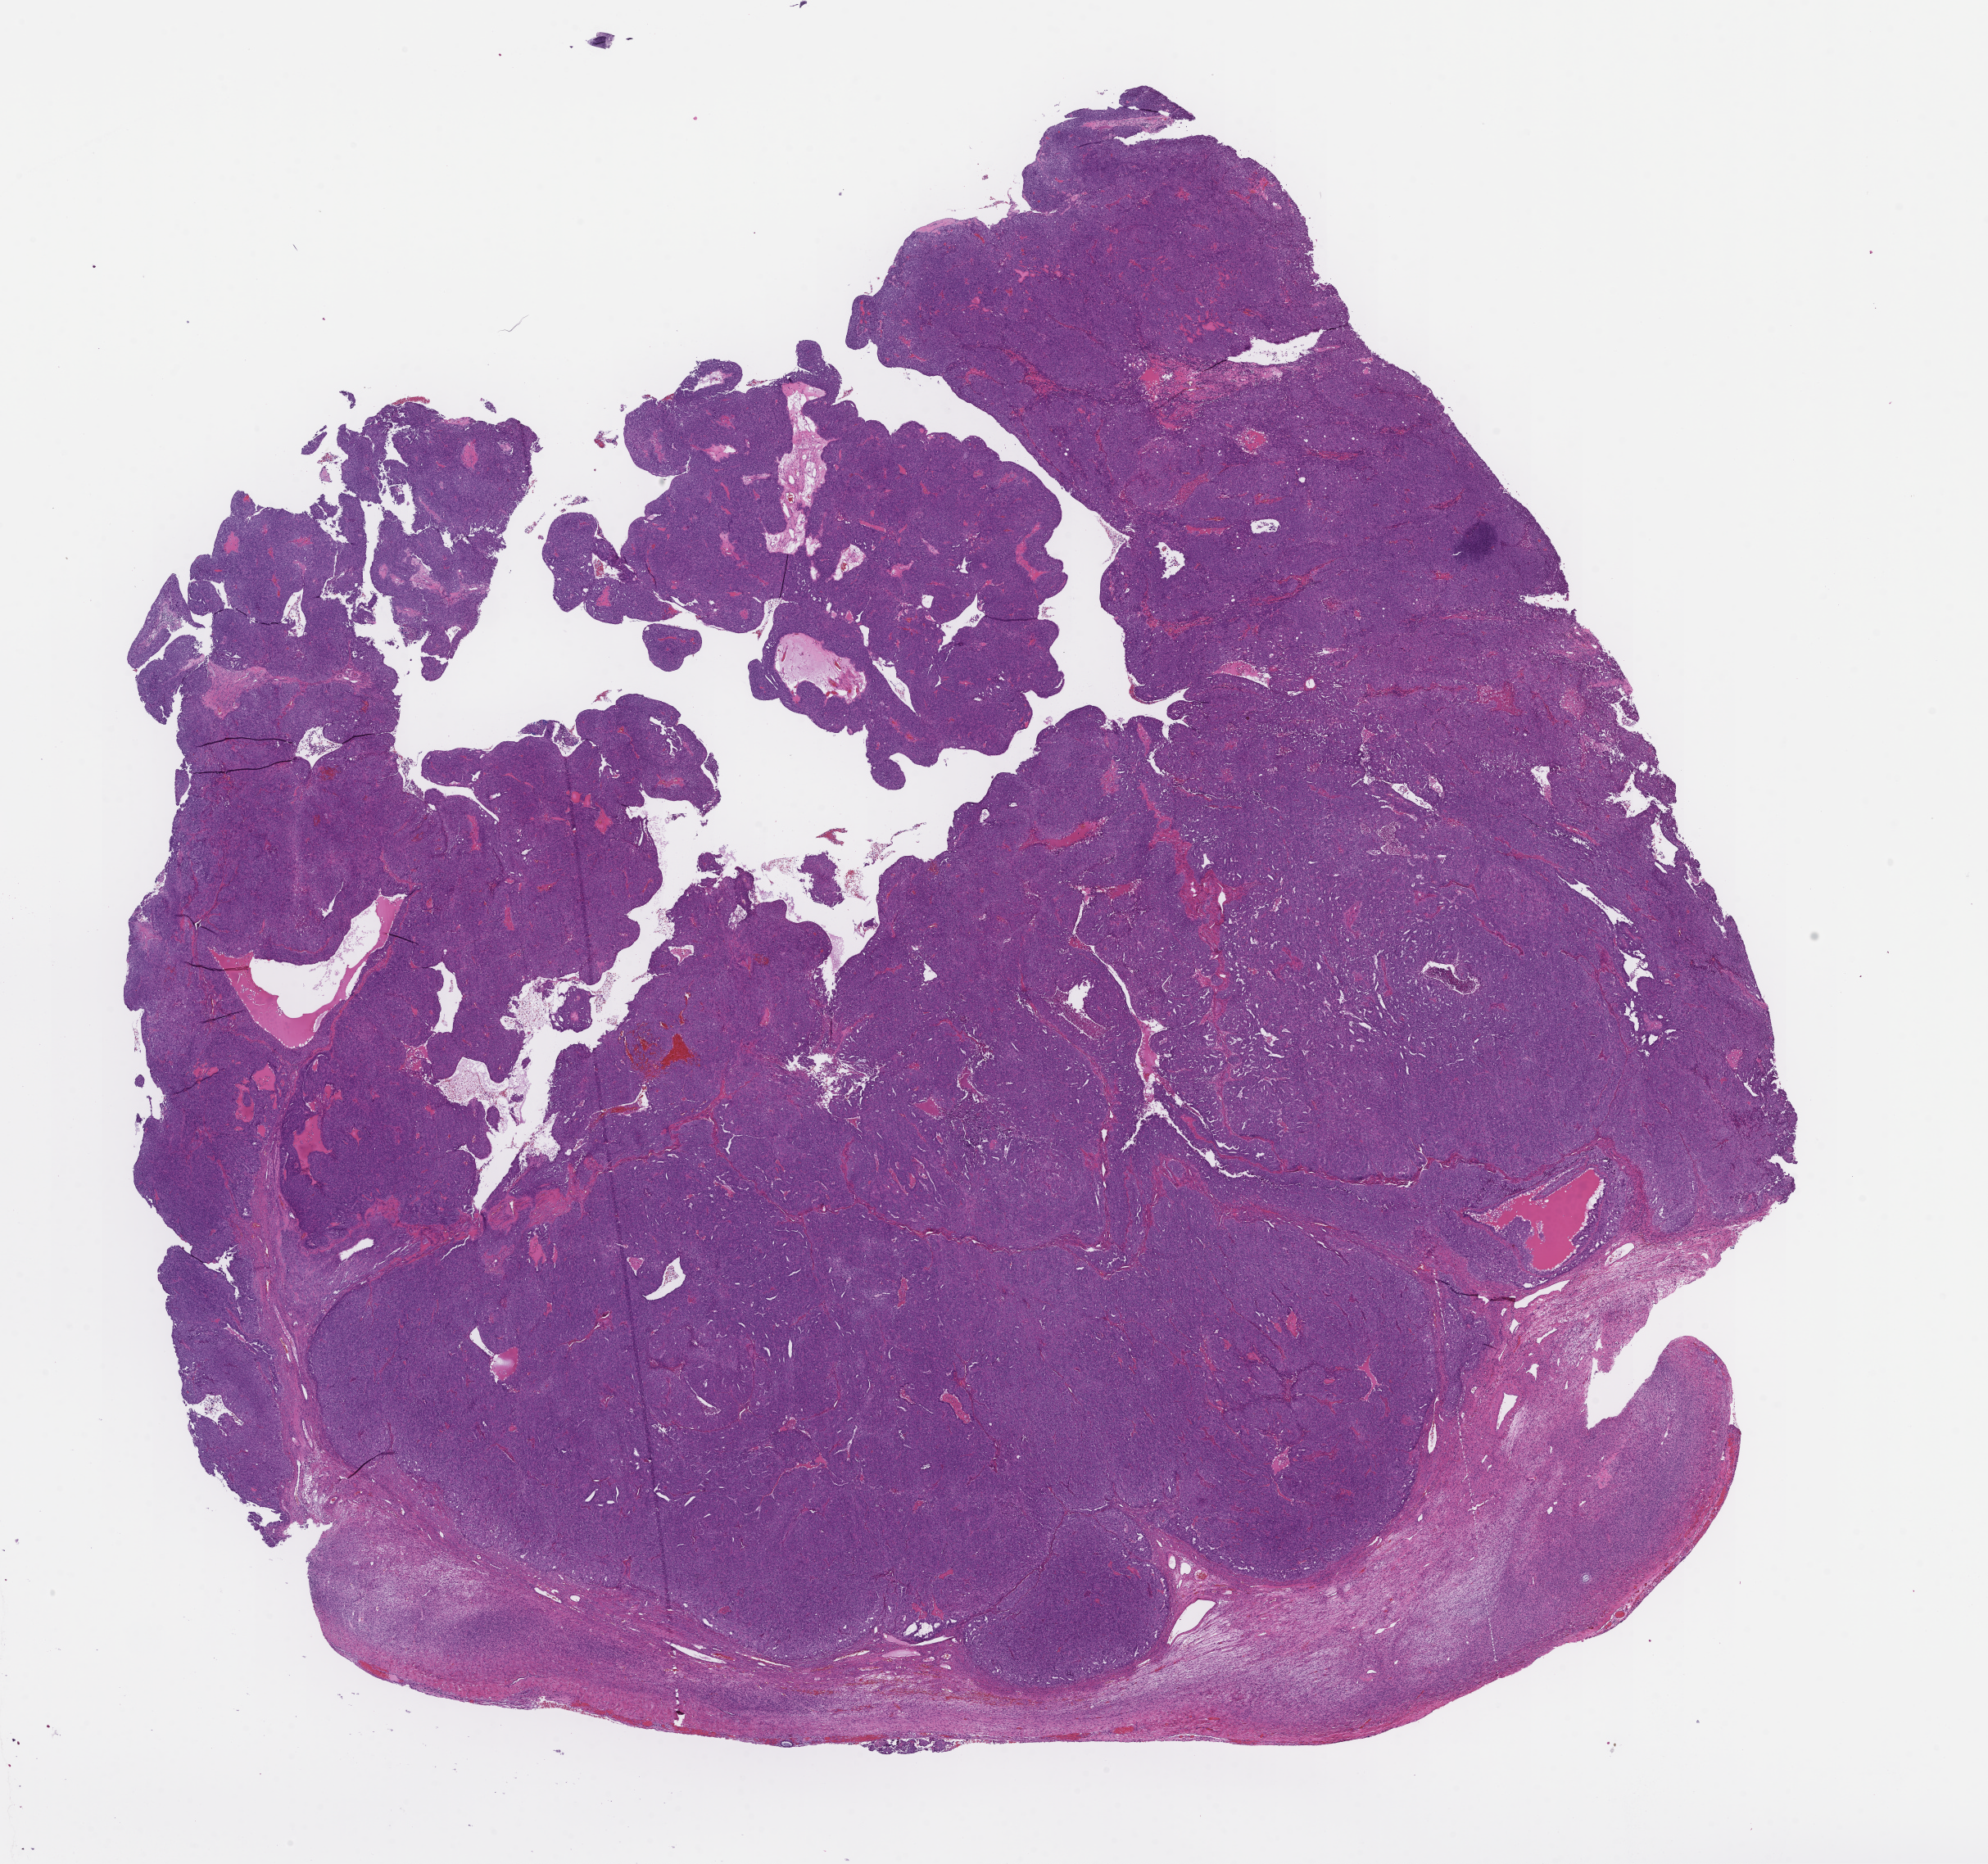
Digitized H&E-stained section, a low-resolution overview of the entire scanned area, about 19.6 x 18.4 mm, formalin-fixed, paraffin-embedded (FFPE) tissue, site: ovary. Patient sex: female.
This section: primary tumor. Diagnosis: Ovarian Carcinoma.